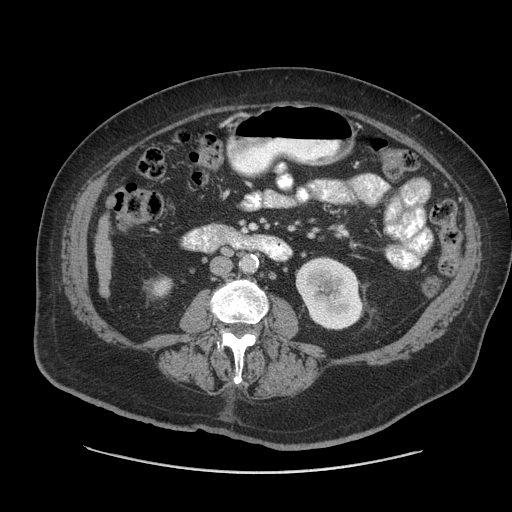
Contrast-enhanced abdominal CT (liver protocol), one axial slice. Position 10 of 91 along the scan axis. 140 kVp. Soft-tissue window (W 400 / L 40 HU). 2.5 mm slice thickness. 512 × 512 image matrix. From the clinical record (not read from this slice): diagnosis: hepatocellular carcinoma (patient treated with transarterial chemoembolisation; whether this scan precedes or follows treatment is not stated here); TNM stage (as recorded): Stage-I; Child-Pugh class: A; tumour differentiation: well differentiated; tumour nodularity: uninodular.
Annotated regions visible in this slice (semi-automatically segmented with operator editing):
- liver parenchyma outside the tumour (the mass and vessels are separate outlines, so this box may not span the whole liver): box from (x=94, y=216) to (x=112, y=295) px